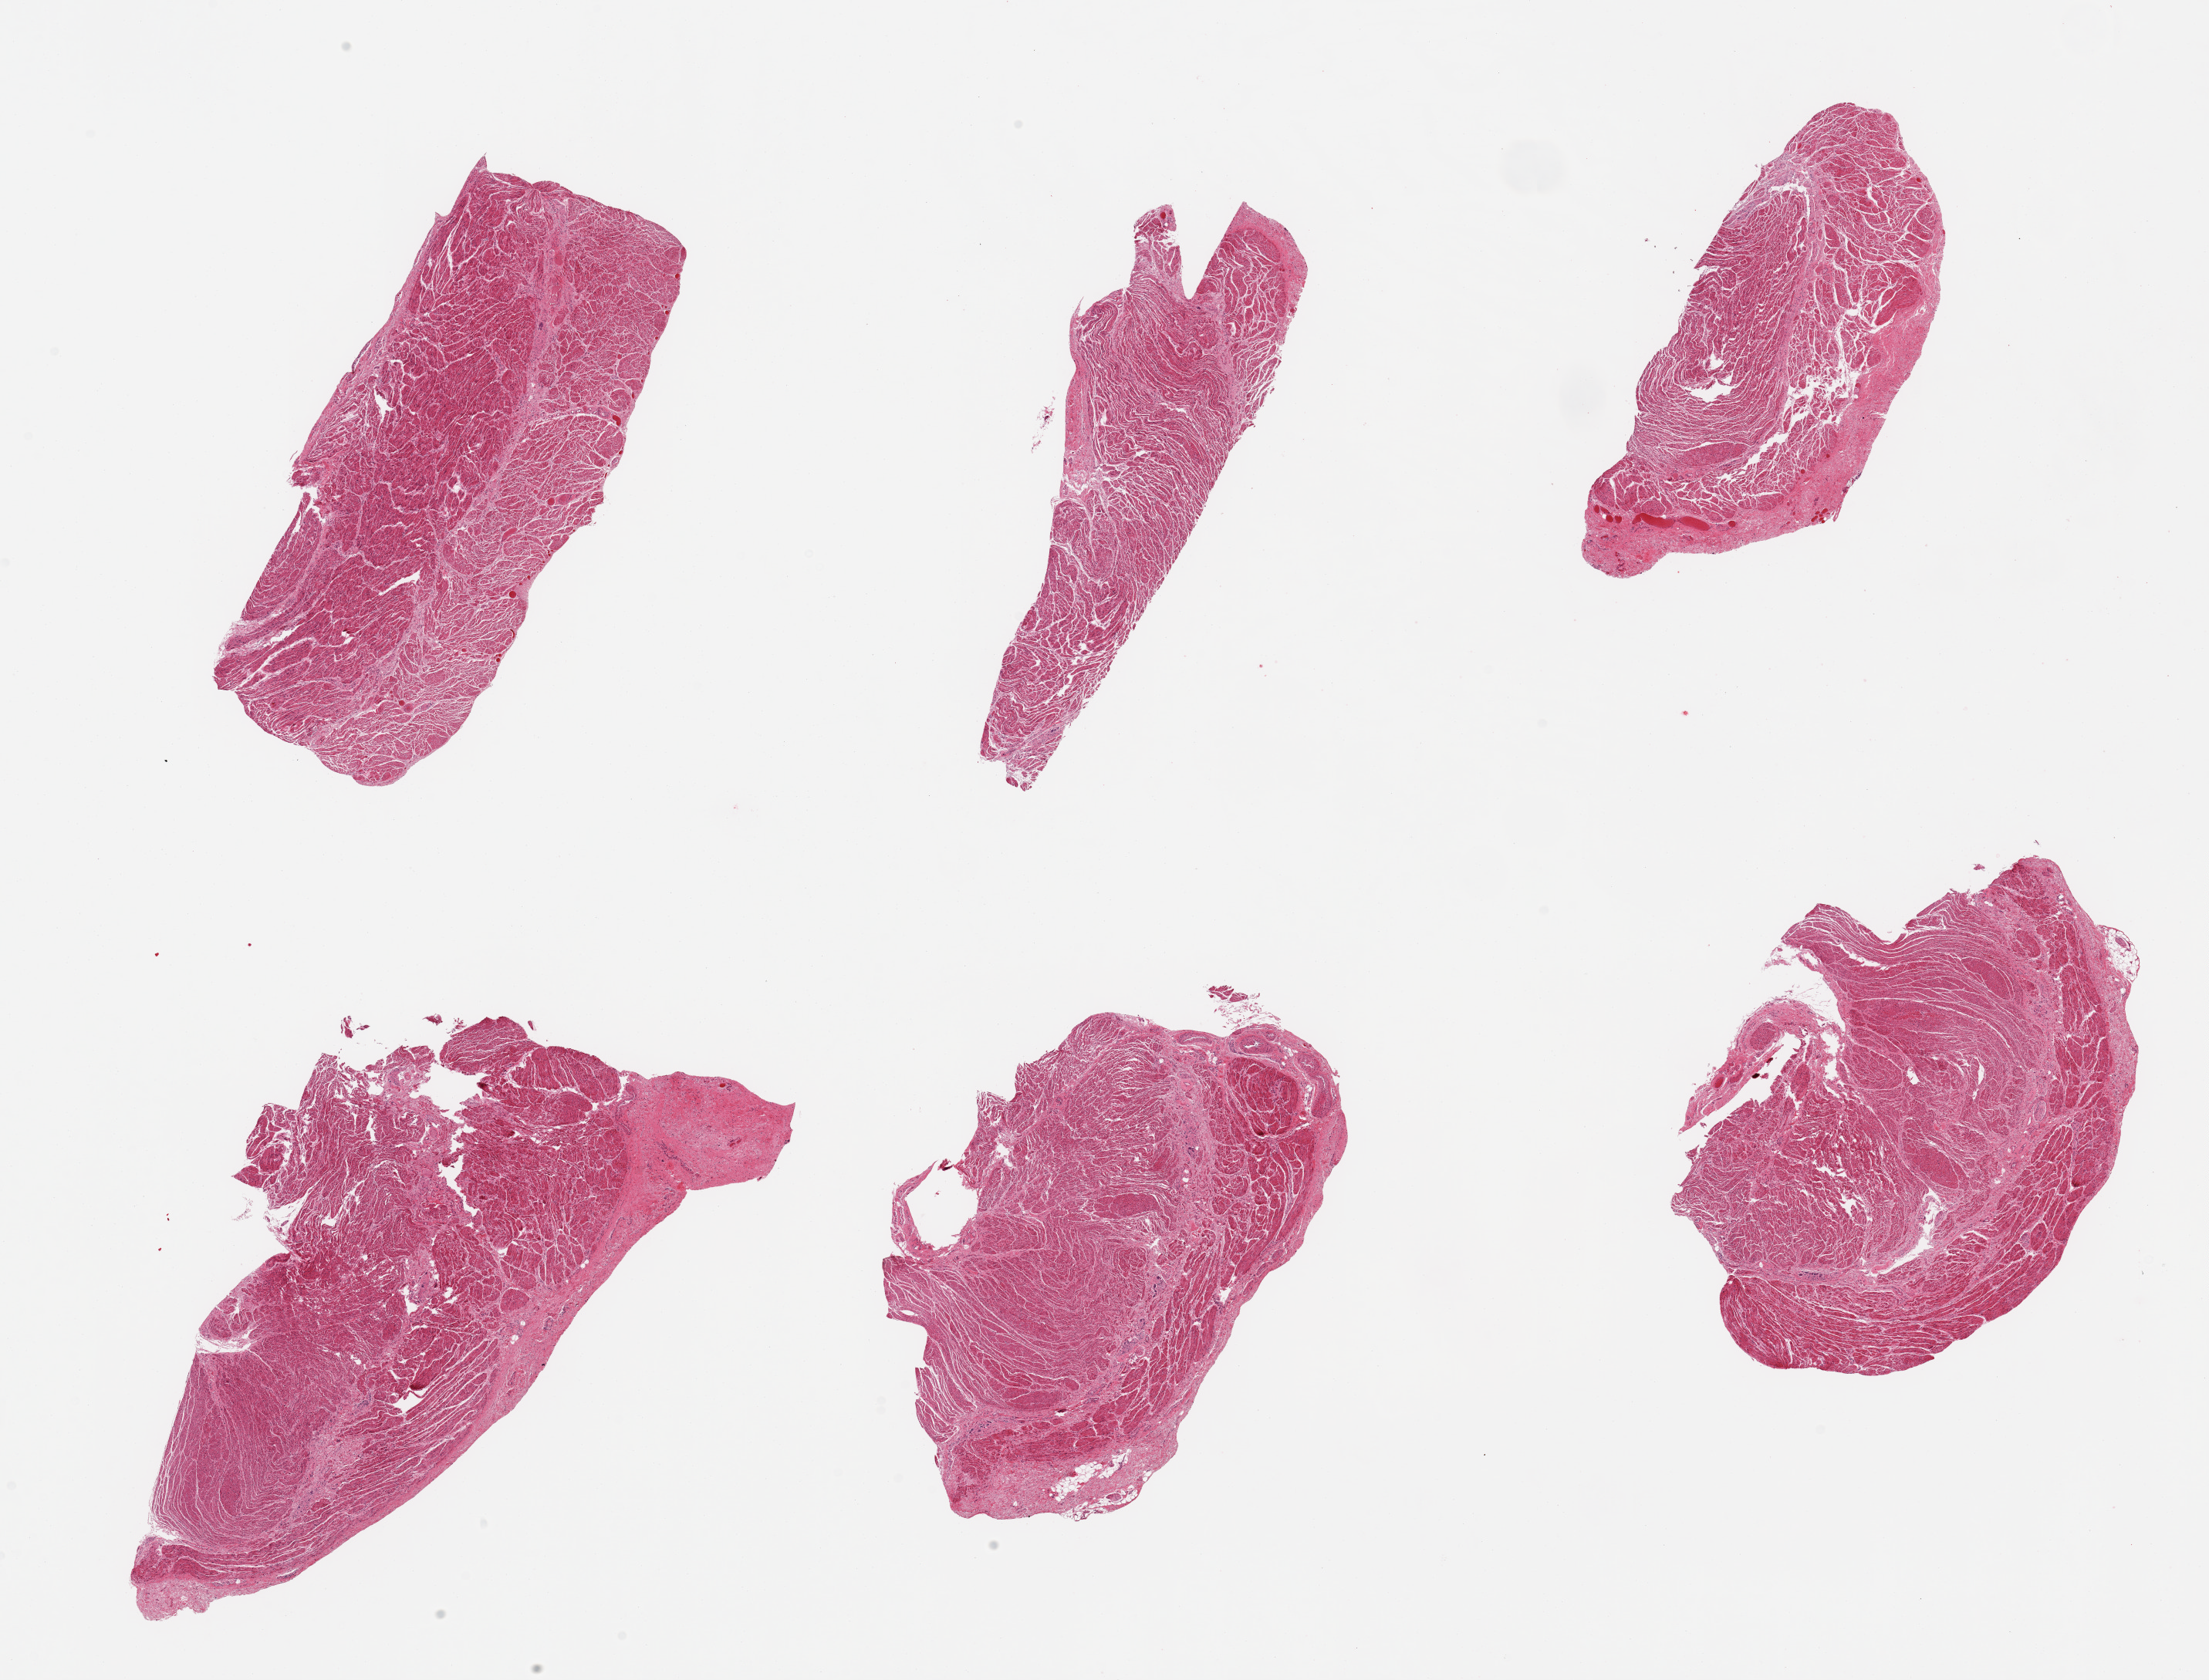
Whole-slide image, haematoxylin and eosin stain, shown as a low-resolution overview of the whole scanned area (about 22.6 x 17.2 mm, slide scanned at 20x), PAXgene-fixed paraffin-embedded (PFPE) section, target tissue: gastroesophageal junction, tissue donor sample. Female donor.
Review note (as recorded): 6 pieces; well dissected muscle.